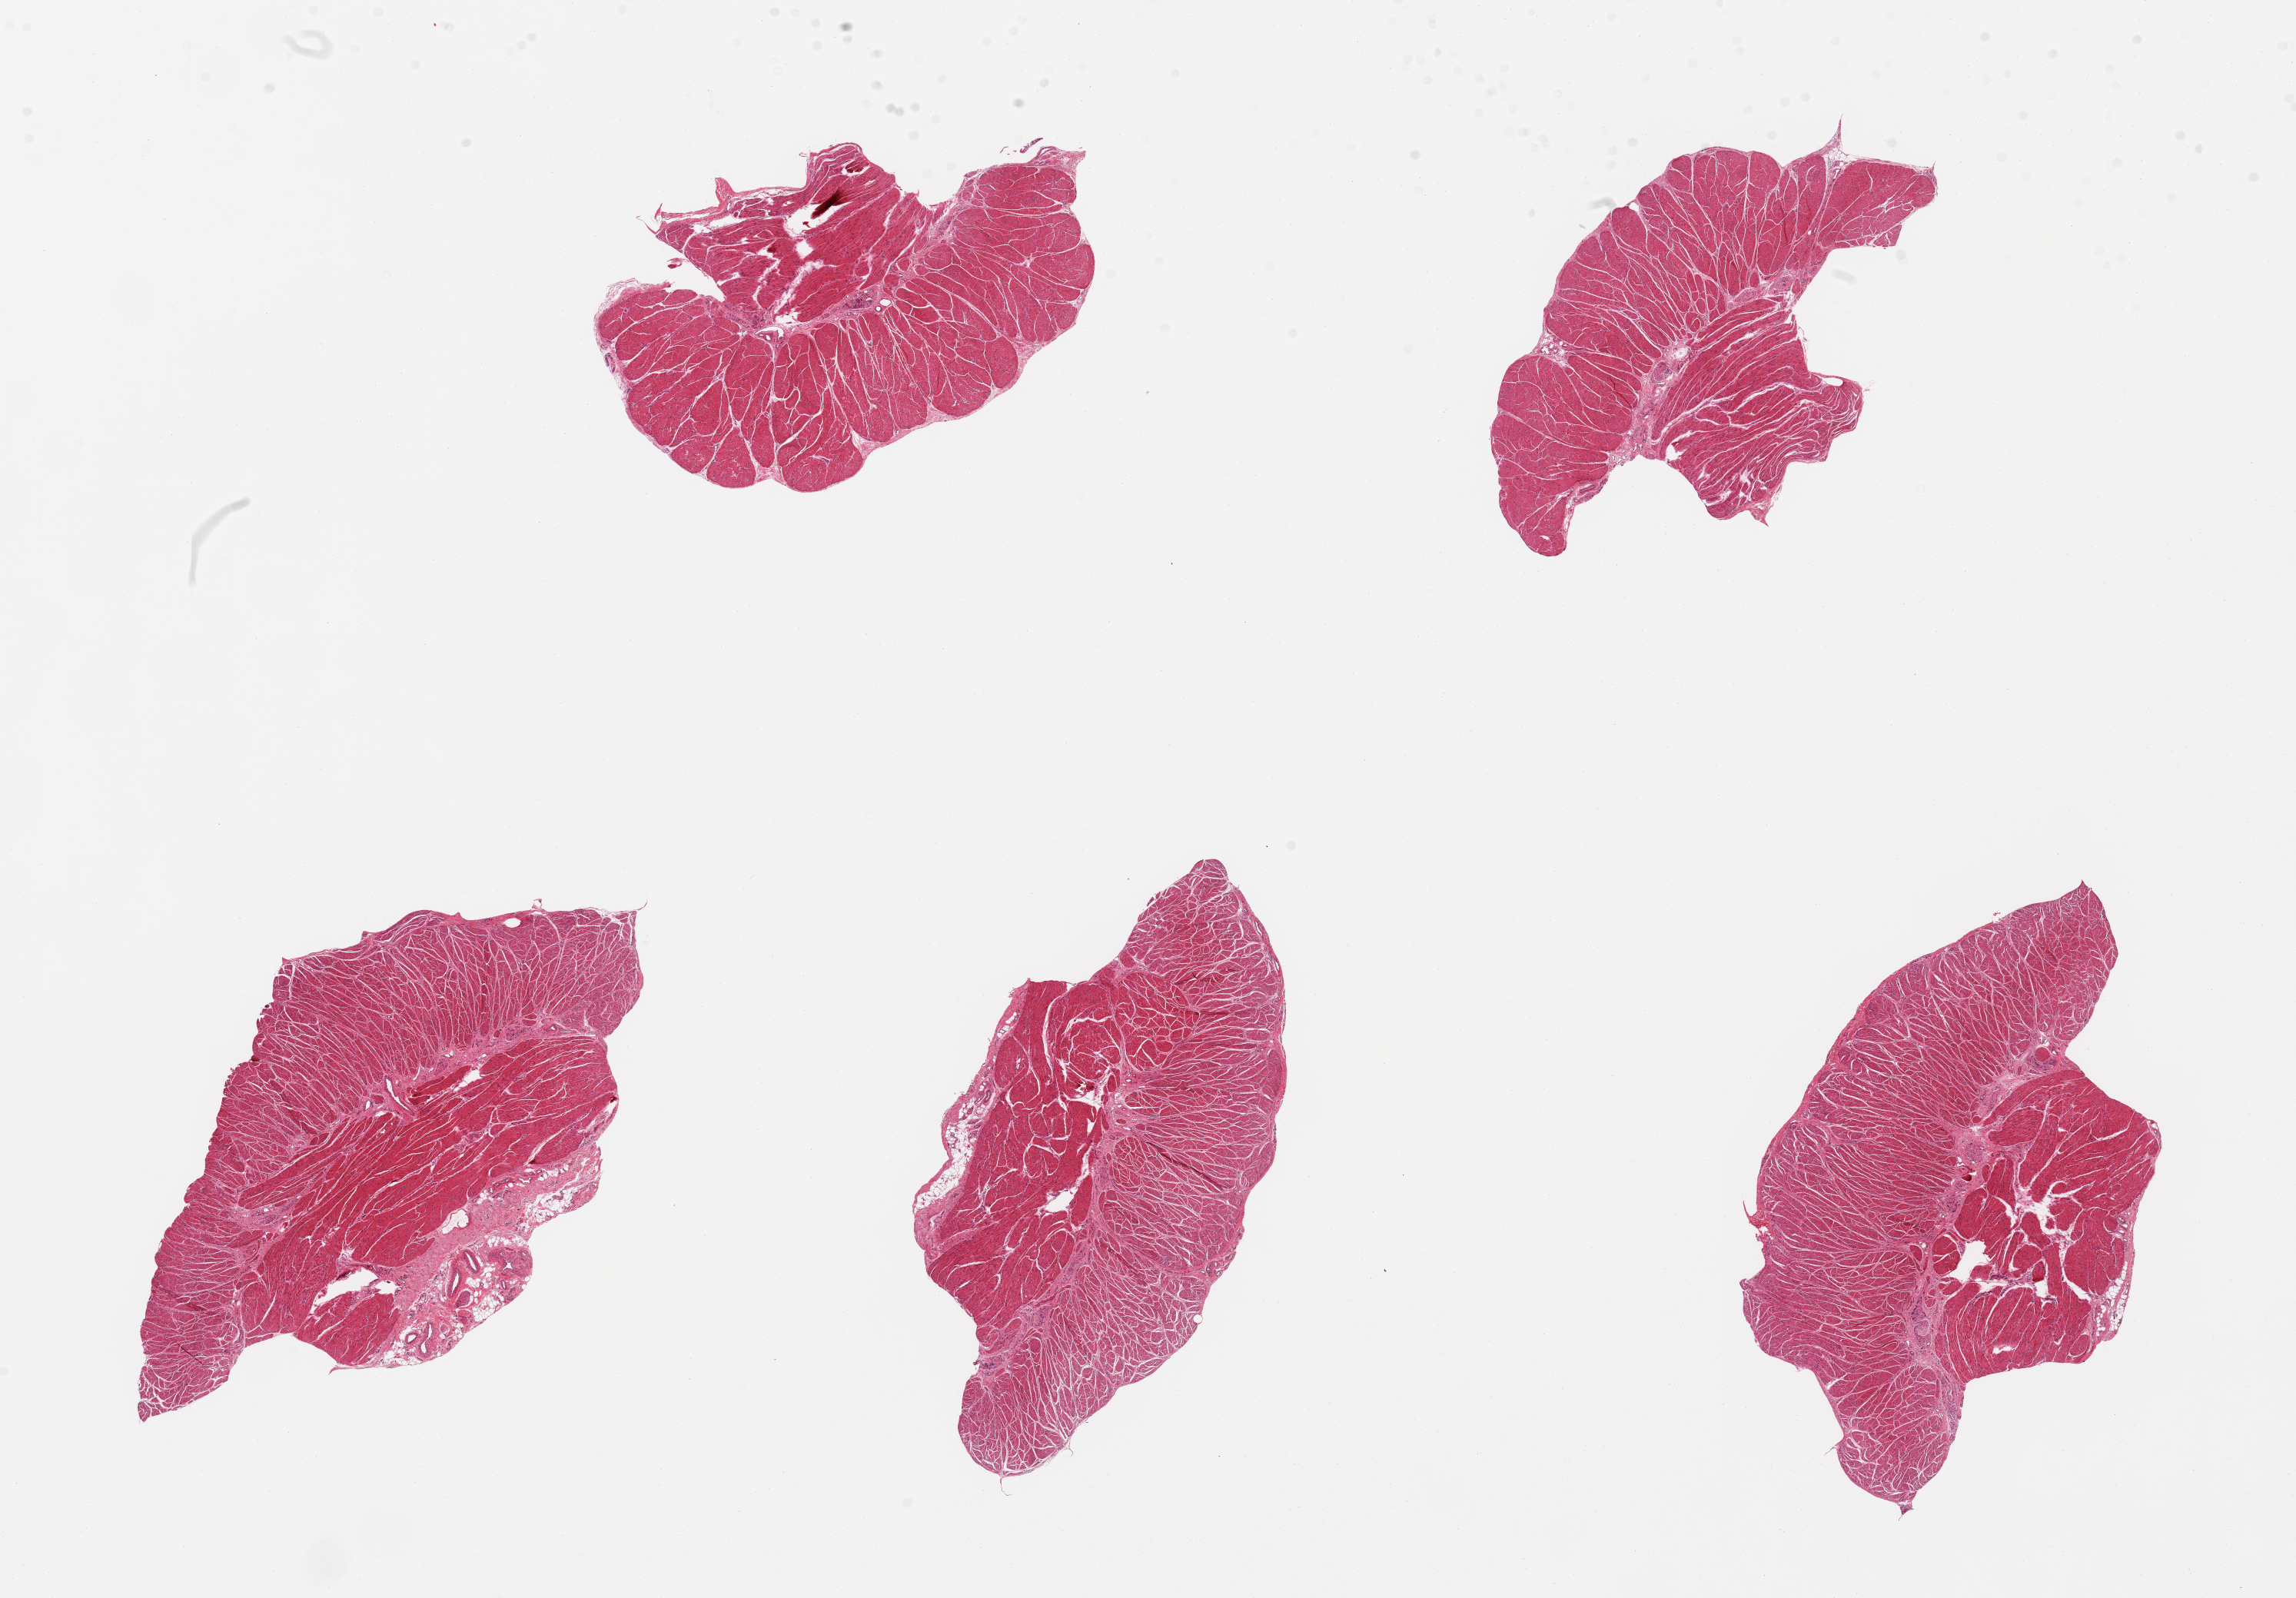
Digitized haematoxylin and eosin-stained section, a low-resolution overview of the entire scanned area, about 23.6 x 16.4 mm (acquisition: 20x scan), PAXgene-fixed, paraffin-embedded tissue, section of gastroesophageal junction (target tissue), donor tissue sample. Donor: male.
• reviewer comment on this tissue sample: 5 pieces, target muscularis obtained